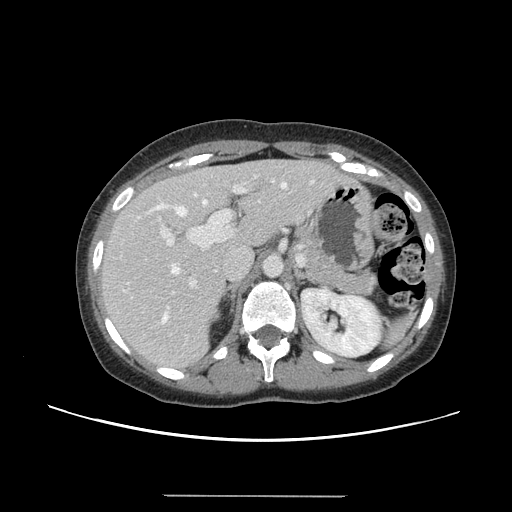
Contrast-enhanced abdominal CT, one axial slice. Slice 90 of 144 in the series (ordered by position). 120 kVp. Intravenous contrast given. Soft-tissue window (W 400 / L 40 HU). 512 × 512 image matrix, field of view 380 × 380 mm. Female patient, age 53 years. Case-level facts recorded for this patient, not image findings: diagnosis: colorectal cancer liver metastases, imaged before liver resection; multiple liver metastases: yes.
Annotated regions visible in this slice (outlined manually by an expert reader):
- hepatic veins: bounding box (x1, y1, x2, y2) in pixels: (152, 181, 313, 323)
- liver: (101, 160, 344, 370)
- planned liver remnant (the part of the liver to remain after resection): (101, 160, 313, 297)
- portal vein (with intrahepatic branches): (158, 179, 275, 288)